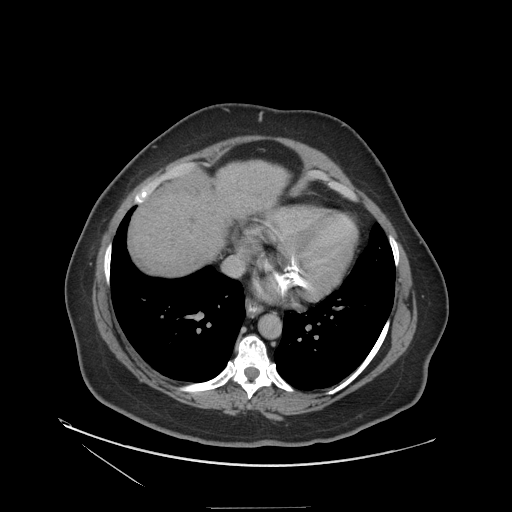
Contrast-enhanced abdominal CT (liver protocol), one axial slice. Position 106 of 127 along the scan axis. Reconstruction kernel STANDARD. 140 kVp. Soft-tissue window (W 400 / L 40 HU). 2.5 mm slice thickness. 512 × 512 image matrix. Case-level facts recorded for this patient, not image findings: diagnosis: hepatocellular carcinoma (patient treated with transarterial chemoembolisation; whether this scan precedes or follows treatment is not stated here); TNM stage (as recorded): Stage-II; Child-Pugh class: A; tumour nodularity: multinodular; tumour size: 3 cm.
Annotated regions visible in this slice (semi-automatically segmented with operator editing):
- liver parenchyma outside the tumour (the mass and vessels are separate outlines, so this box may not span the whole liver): bounding box <128,160,286,274> (left, top, right, bottom; pixels)
- liver vessels: <170,165,187,176>